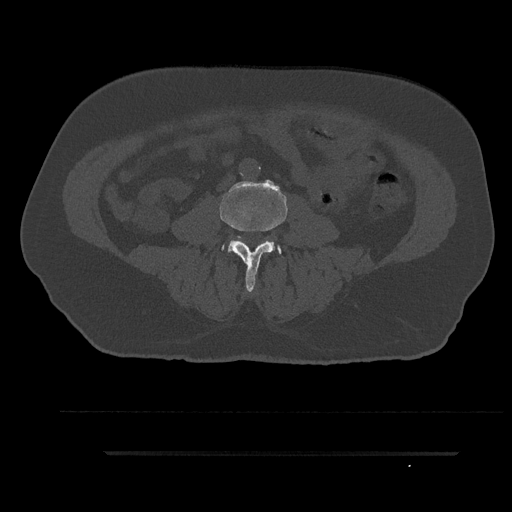
CT including the spine, one axial slice; slice 21 of 797 in the series (ordered by position); reconstruction kernel Br40s/3; bone window (W 1800 / L 400 HU); 0.5 mm slice thickness; 512 × 512 image matrix, field of view 432 × 432 mm. Male patient, age 63 years. From the clinical record (not read from this slice): primary cancer: renal; vertebrae with lytic lesions (as recorded): T8.
Outlined on this slice (semi-automatic segmentation, software-assisted and operator-edited):
- L3 vertebra: bounding box <219,185,288,293> (left, top, right, bottom; pixels)
- L4 vertebra: <221,241,282,254>